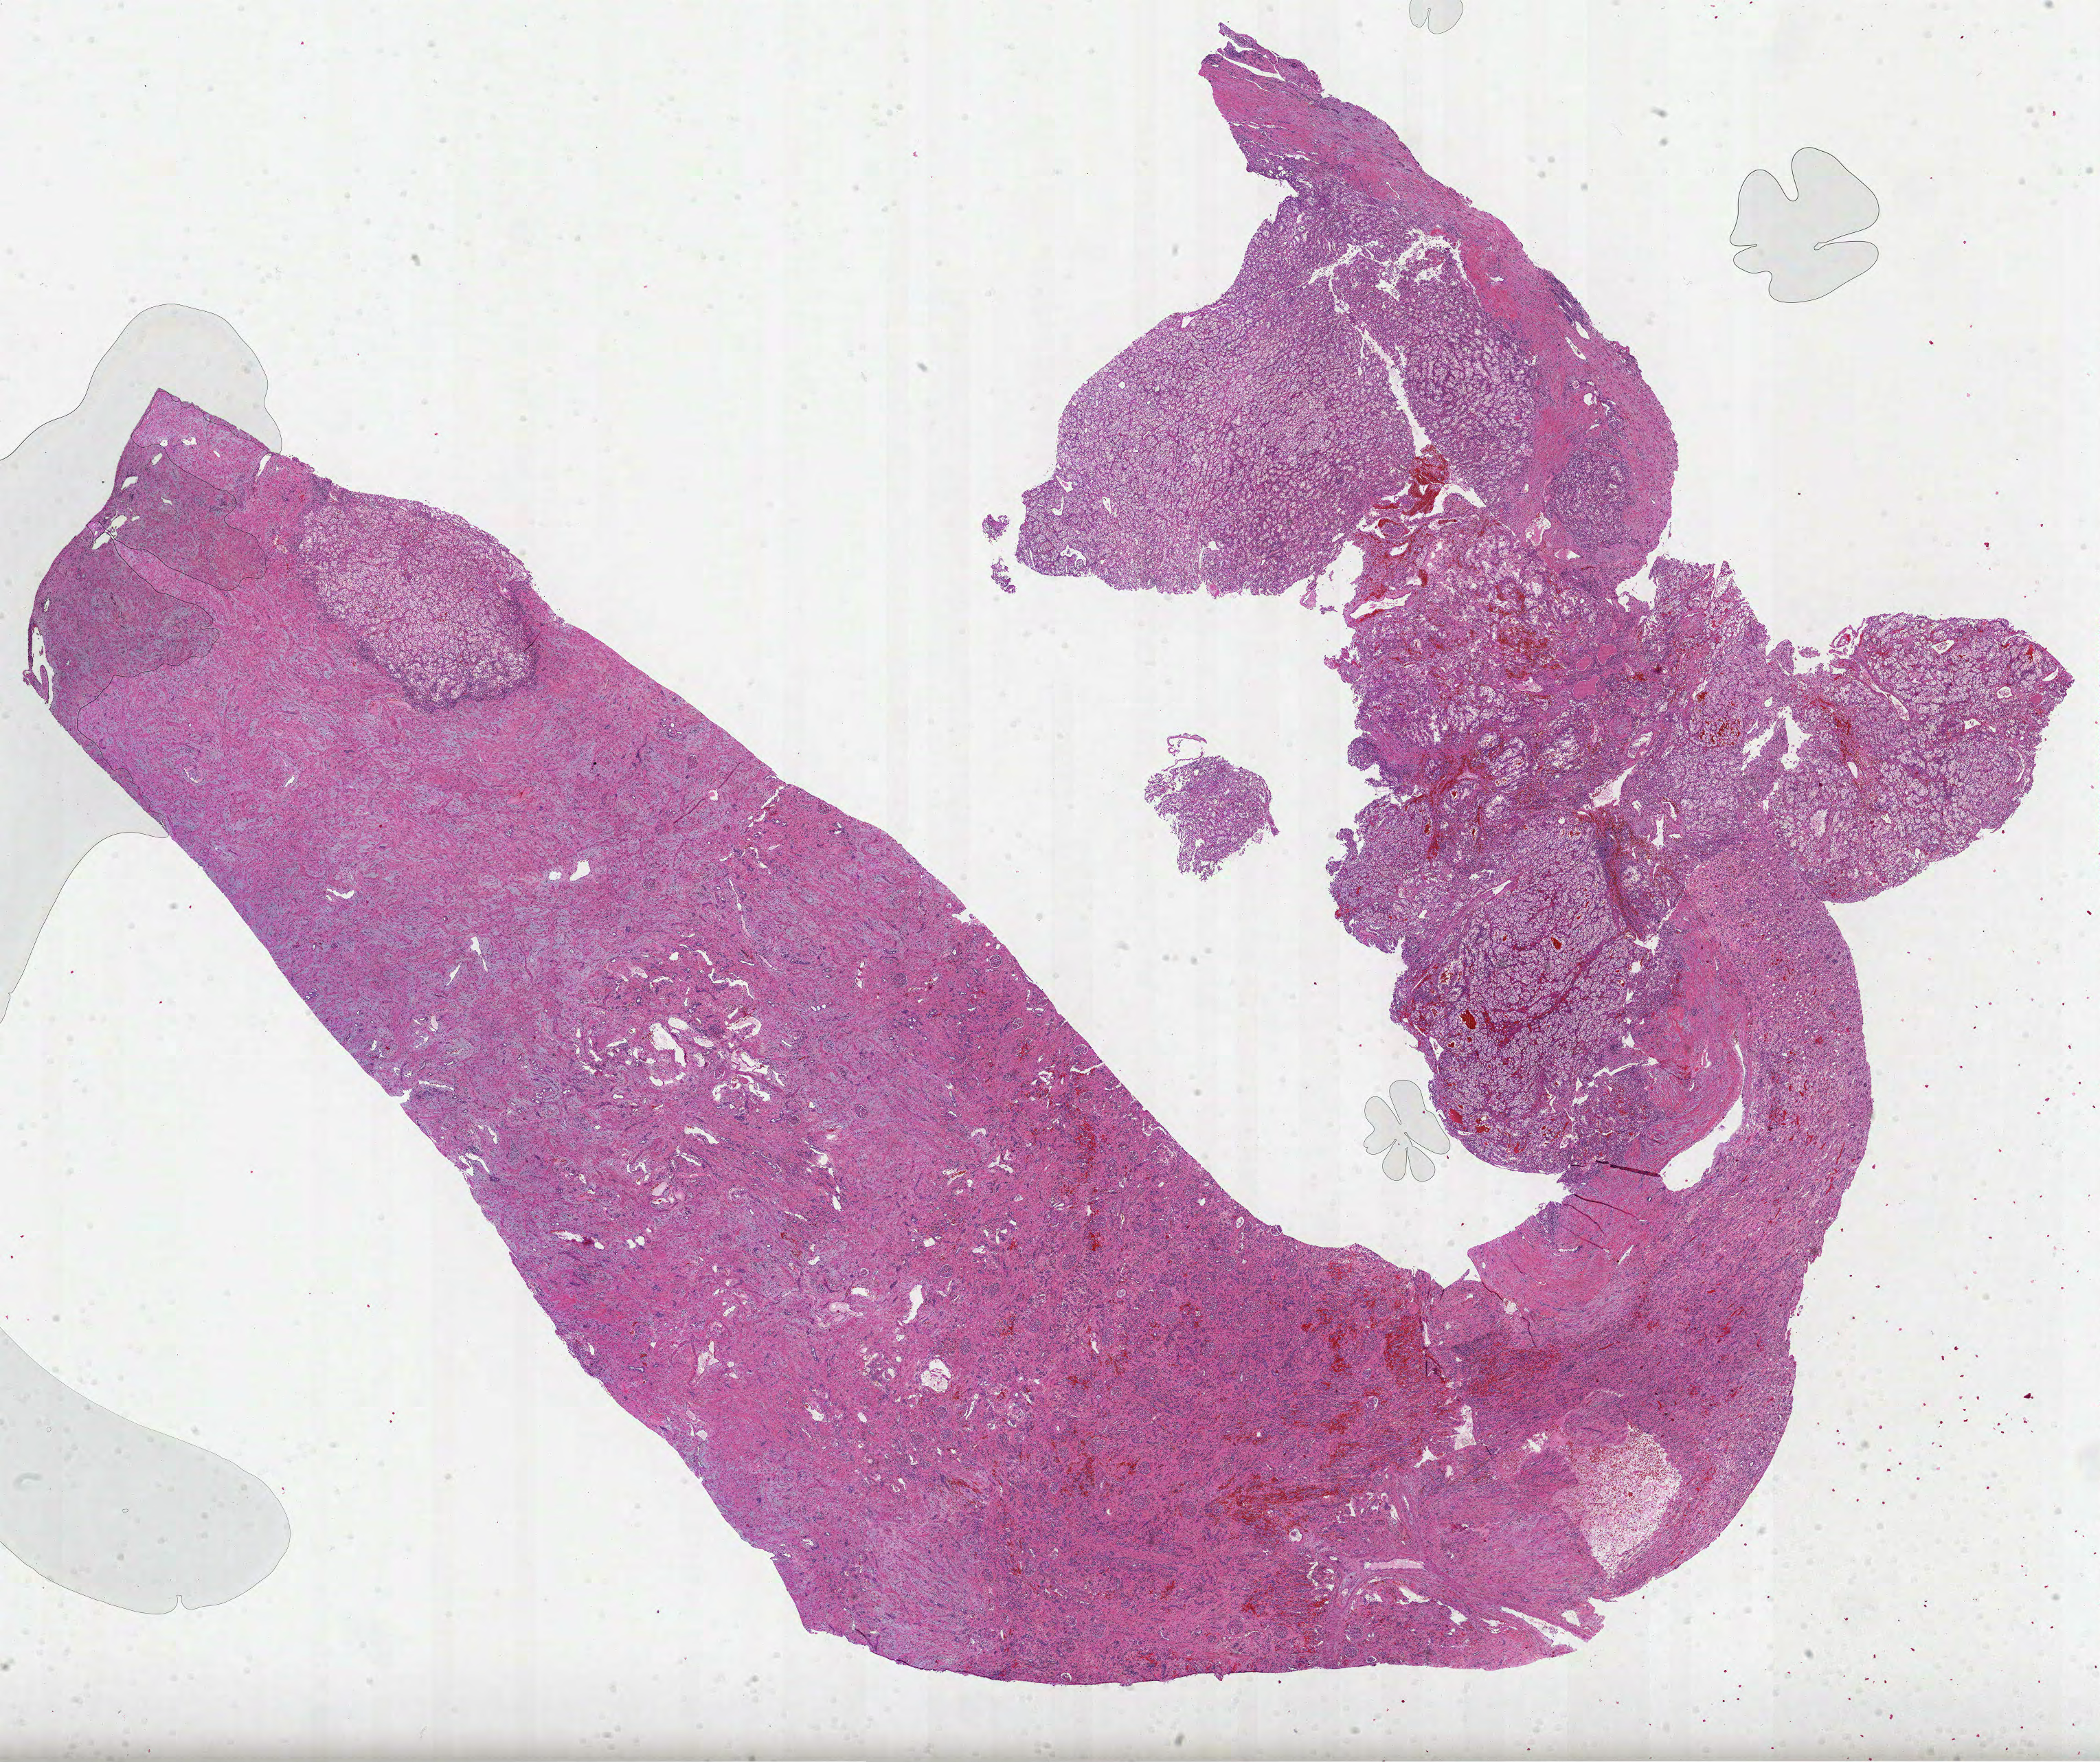
Whole-slide histology image, H&E-stained — low-resolution overview of the scanned area, about 24.7 x 20.7 mm (from a 40x scan); FFPE section; sample: primary tumour, kidney. Patient: male, age at initial diagnosis 26 years. Histologic grade: G2 (moderately differentiated).
* laterality: right
* AJCC pathologic stage: I
* histologic diagnosis: Clear cell adenocarcinoma, NOS
* TNM: T1a NX M0